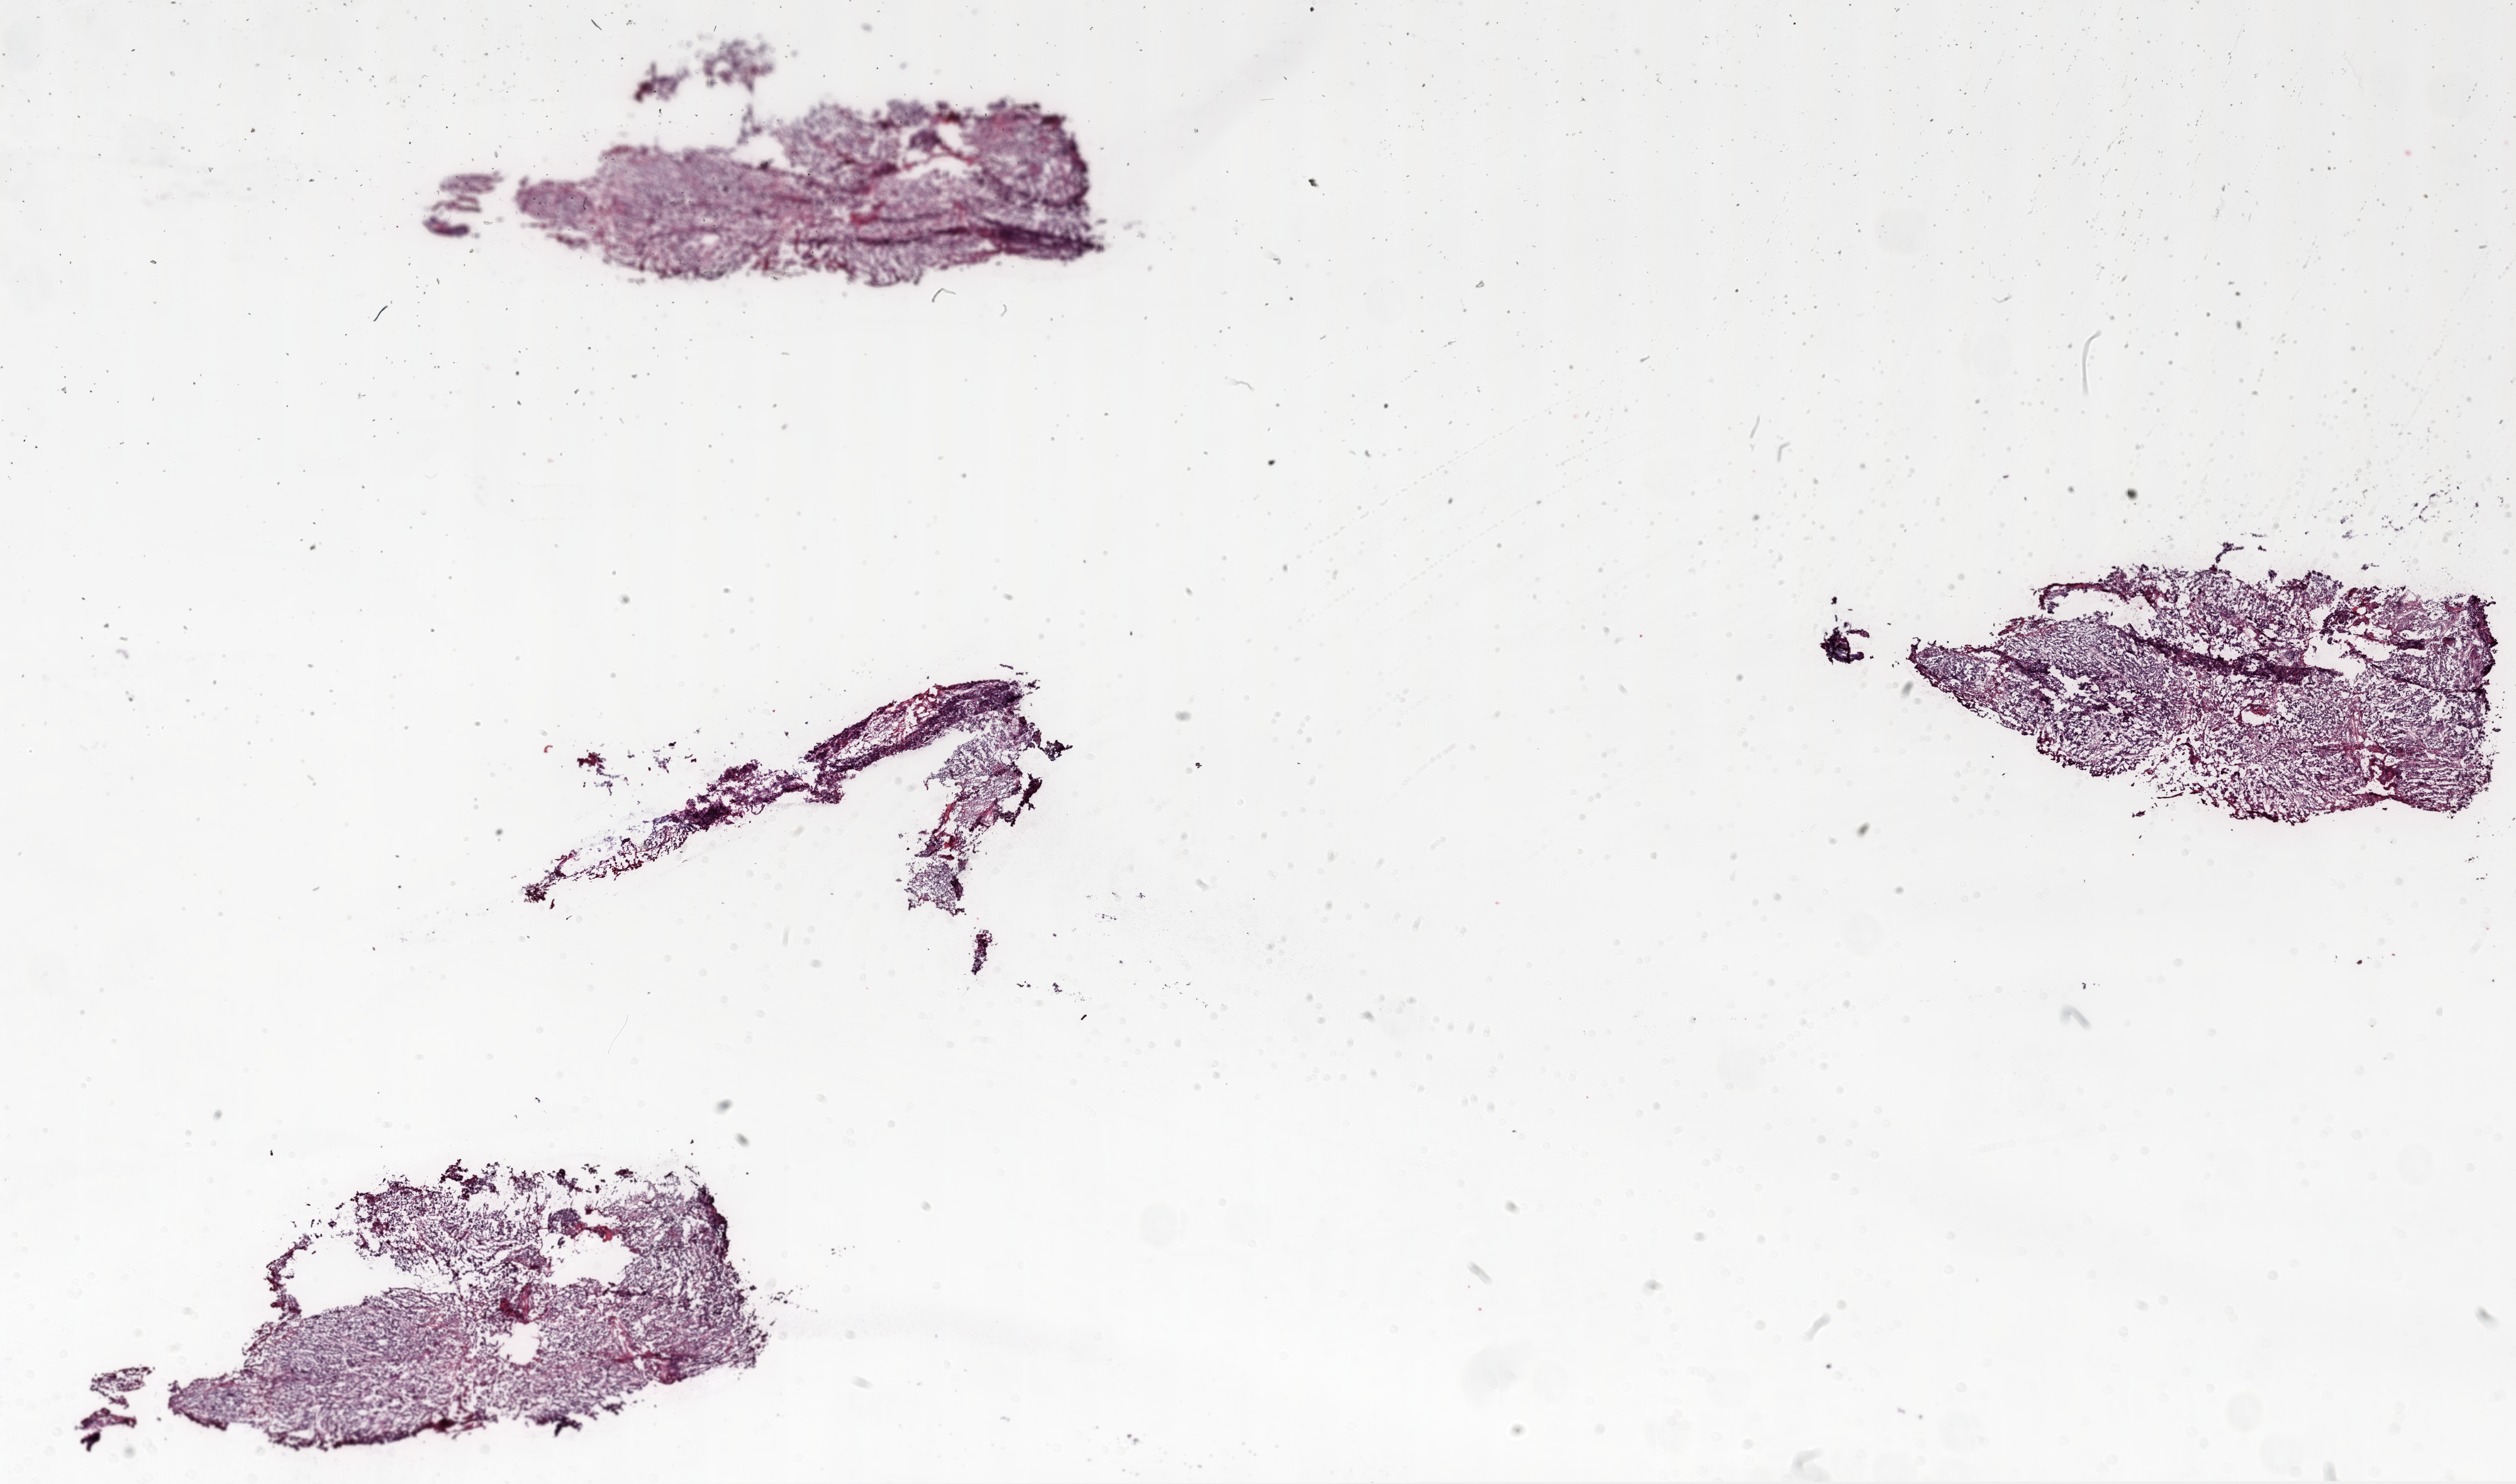
H&E-stained whole-slide image, a low-resolution overview of the entire scanned area, about 32.1 x 18.9 mm. Frozen section from the top of the tissue portion. Primary tumour sample from the ovary. Female, age 56 years at initial diagnosis. Histologic grade: G3 (poorly differentiated). Composition of this section per pathologist review: tumour cells 90%, tumour nuclei 95%, normal cells 0%, stromal cells 10%, necrosis 0%.
Pathologic diagnosis: Serous cystadenocarcinoma, NOS. FIGO stage: IIIC.